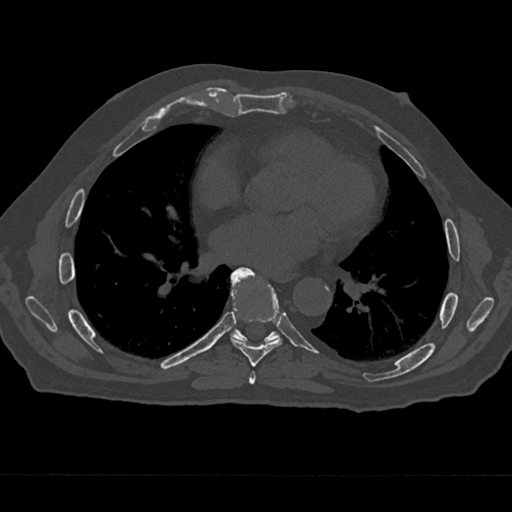
CT including the spine, one axial slice. Position 352 of 797 along the scan axis. Reconstruction kernel Br40s/3. 120 kVp. Bone window (W 1800 / L 400 HU). 0.5 mm slice thickness. 512 × 512 image matrix. Patient: male, 75 years. Case-level facts recorded for this patient, not image findings: primary cancer: renal; vertebrae with lytic lesions (as recorded): T4.
Outlined on this slice (semi-automatically segmented with operator editing):
- T6 vertebra: bounding box <249,371,256,385> (left, top, right, bottom; pixels)
- T7 vertebra: <230,267,283,367>
- T8 vertebra: <230,275,280,343>